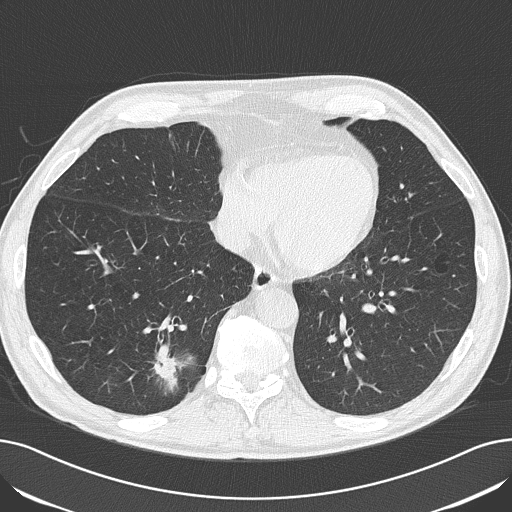
Low-dose screening chest CT, one axial slice. Slice 59 of 182 in the series (ordered by position). Reconstruction kernel B50f. 120 kVp. Lung window (W 1500 / L -600 HU). 512 × 512 image matrix, field of view 368 × 368 mm.
Structures marked on this image (outlined manually by an expert reader):
- lesion 1 (tumor, lower lobe of right lung): box from (x=153, y=358) to (x=181, y=389) px